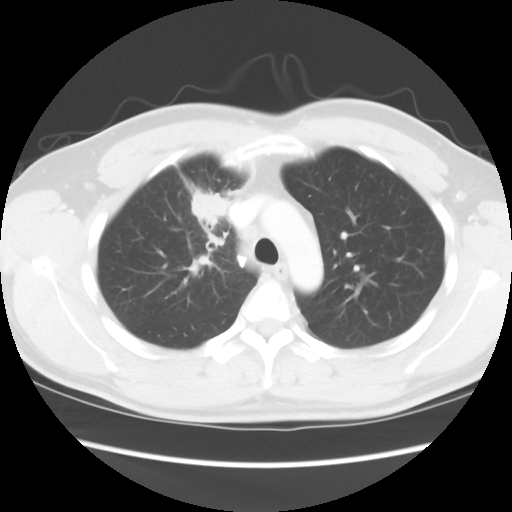
Chest CT, one axial slice. Slice 65 of 80 in the series (ordered by position). Reconstruction kernel STANDARD. 120 kVp. Lung window (W 1500 / L -600 HU). 512 × 512 image matrix, field of view 360 × 360 mm. Patient: male, 35 years. From the clinical record (not read from this slice): clinical TNM (as recorded): T1c N1 M1b.
Outlined on this slice (bounding box drawn by a radiologist):
- lung tumour (recorded histology: adenocarcinoma): bounding box (x1, y1, x2, y2) in pixels: (187, 187, 235, 233)